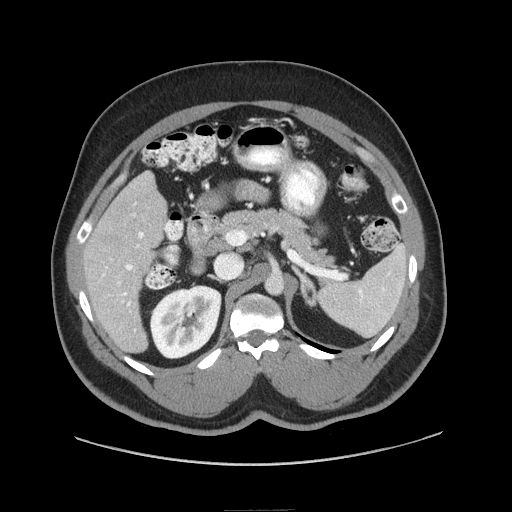
Contrast-enhanced abdominal CT (liver protocol), one axial slice; slice 38 of 87 in the series (ordered by position); reconstruction kernel STANDARD; 140 kVp; soft-tissue window (W 400 / L 40 HU); 2.5 mm slice thickness; 512 × 512 image matrix, field of view 440 × 440 mm. Case-level facts recorded for this patient, not image findings: diagnosis: hepatocellular carcinoma (patient treated with transarterial chemoembolisation; whether this scan precedes or follows treatment is not stated here); TNM stage (as recorded): Stage-II; Child-Pugh class: A; tumour differentiation: moderately differentiated; tumour nodularity: uninodular.
Annotated regions visible in this slice (semi-automatic segmentation, software-assisted and operator-edited):
- liver parenchyma outside the tumour (the mass and vessels are separate outlines, so this box may not span the whole liver): bounding box (x1, y1, x2, y2) in pixels: (84, 172, 166, 352)
- liver vessels: (102, 203, 144, 306)